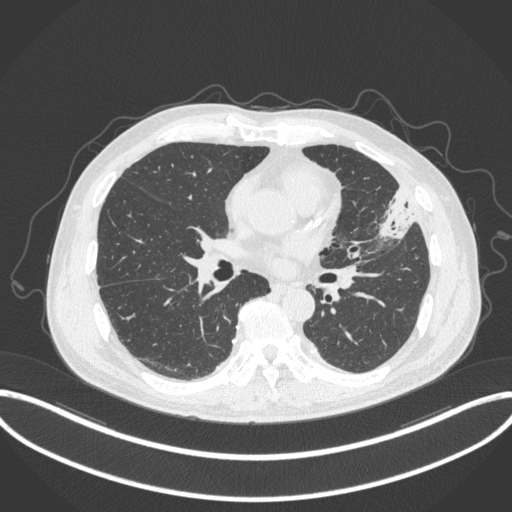
Chest CT, one axial slice; position 163 of 382 along the scan axis; reconstruction kernel B31f; 120 kVp; lung window (W 1500 / L -600 HU); 512 × 512 image matrix, field of view 415 × 415 mm. Male patient, age 64 years. From the clinical record (not read from this slice): clinical TNM (as recorded): T4 N1 M0; histopathological grade: G3.
Annotated regions visible in this slice (bounding box drawn by a radiologist):
- lung tumour (recorded histology: adenocarcinoma): box from (x=373, y=184) to (x=416, y=245) px